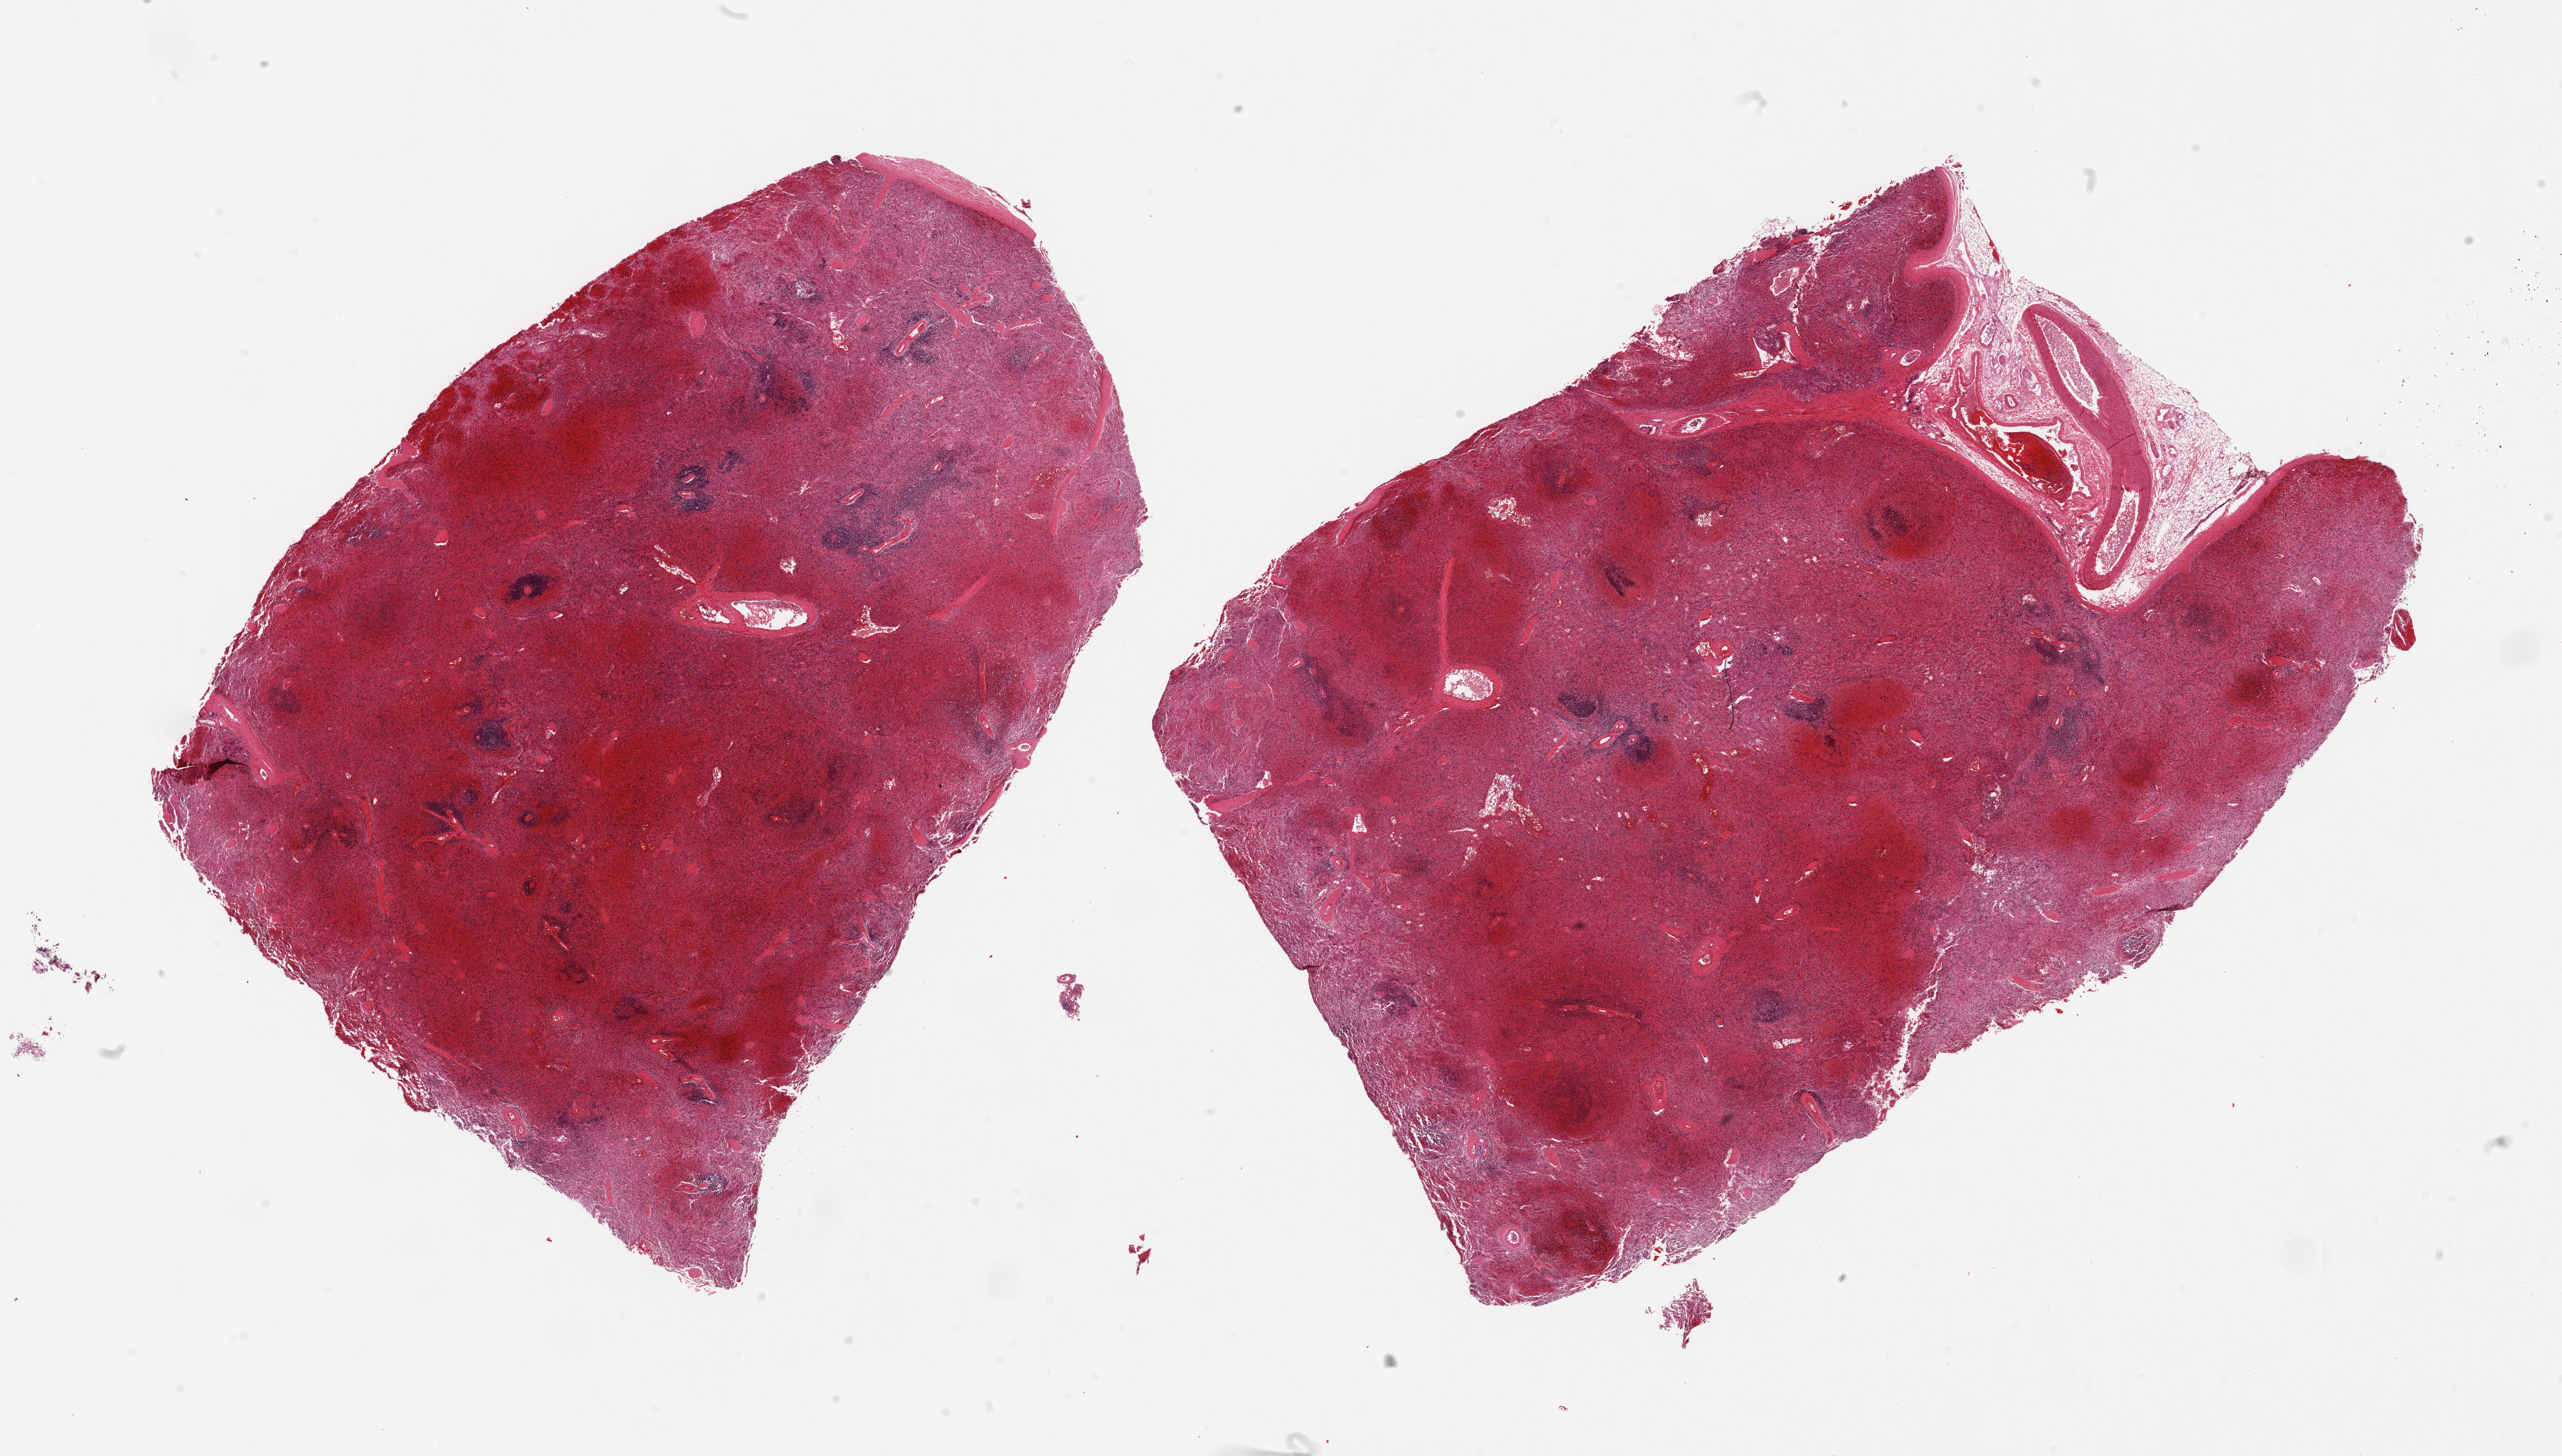
Whole-slide image, haematoxylin and eosin stain — low-resolution overview of the scanned area, about 31.5 x 17.9 mm; PAXgene-fixed, paraffin-embedded tissue; section of spleen (target tissue); tissue donor sample.
Reviewer comment on this tissue sample: 2 pieces; over-sized, congested.